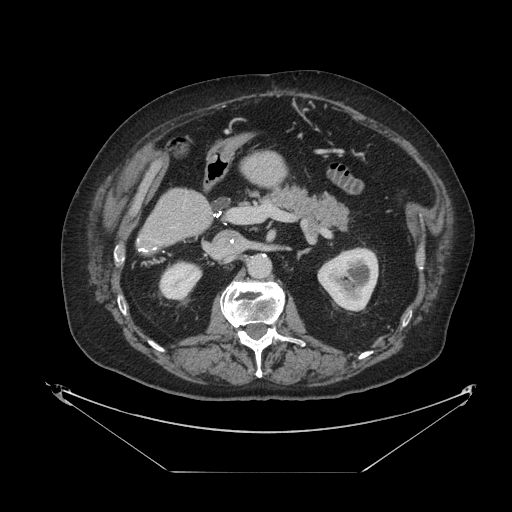
Contrast-enhanced abdominal CT, one axial slice; position 43 of 121 along the scan axis; reconstruction kernel STANDARD; 120 kVp; soft-tissue window (W 400 / L 40 HU); 2.5 mm slice thickness; 512 × 512 image matrix. Male patient, age 68 years. From the clinical record (not read from this slice): diagnosis: colorectal cancer liver metastases, imaged before liver resection; multiple liver metastases: no; largest metastasis: 4 cm.
Annotated regions visible in this slice (expert manual segmentation):
- liver: bounding box (x1, y1, x2, y2) in pixels: (140, 152, 286, 250)
- planned liver remnant (the part of the liver to remain after resection): (140, 152, 286, 250)